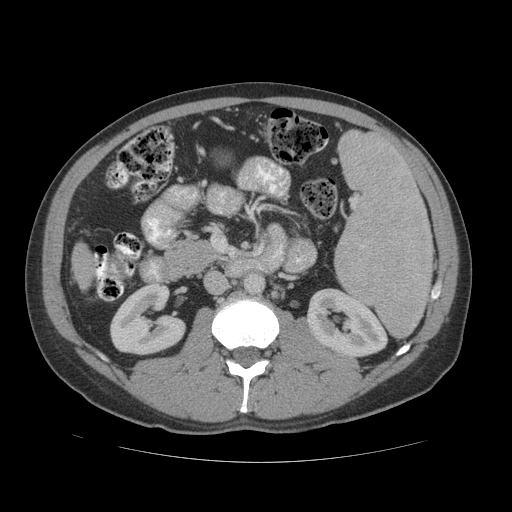
Contrast-enhanced abdominal CT (liver protocol), one axial slice; slice 10 of 81 in the series (ordered by position); soft-tissue window (W 400 / L 40 HU); 2.5 mm slice thickness; 512 × 512 image matrix, field of view 400 × 400 mm. Case-level facts recorded for this patient, not image findings: diagnosis: hepatocellular carcinoma (patient treated with transarterial chemoembolisation; whether this scan precedes or follows treatment is not stated here); TNM stage (as recorded): Stage-IVB; Child-Pugh class: B; tumour differentiation: well differentiated; tumour nodularity: multinodular.
Outlined on this slice (semi-automatically segmented with operator editing):
- liver parenchyma outside the tumour (the mass and vessels are separate outlines, so this box may not span the whole liver): bounding box <72,244,94,288> (left, top, right, bottom; pixels)